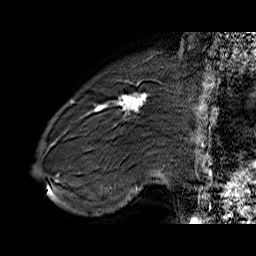
Breast MRI (dynamic contrast-enhanced), one sagittal slice; slice 15 of 60 in the series (ordered by position); dynamic contrast-enhanced series, time point 2 of 6 at this slice position (early post-contrast); 1.5 T; TE 6.4 ms, TR 32.9 ms; 4 mm slice thickness; 256 × 256 image matrix, field of view 200 × 200 mm. Female patient. Case-level facts recorded for this patient, not image findings: setting: breast cancer imaged before/during neoadjuvant chemotherapy; receptor status: HER2-positive.
Structures marked on this image (semi-automatically segmented with operator editing):
- analysis volume of interest (the breast-tissue region the enhancement analysis was run in; not a lesion): bounding box (x1, y1, x2, y2) in pixels: (71, 80, 155, 146)
- tumour enhancement mask (voxels above the 100 % enhancement threshold inside the analysis volume of interest): (71, 93, 147, 115)